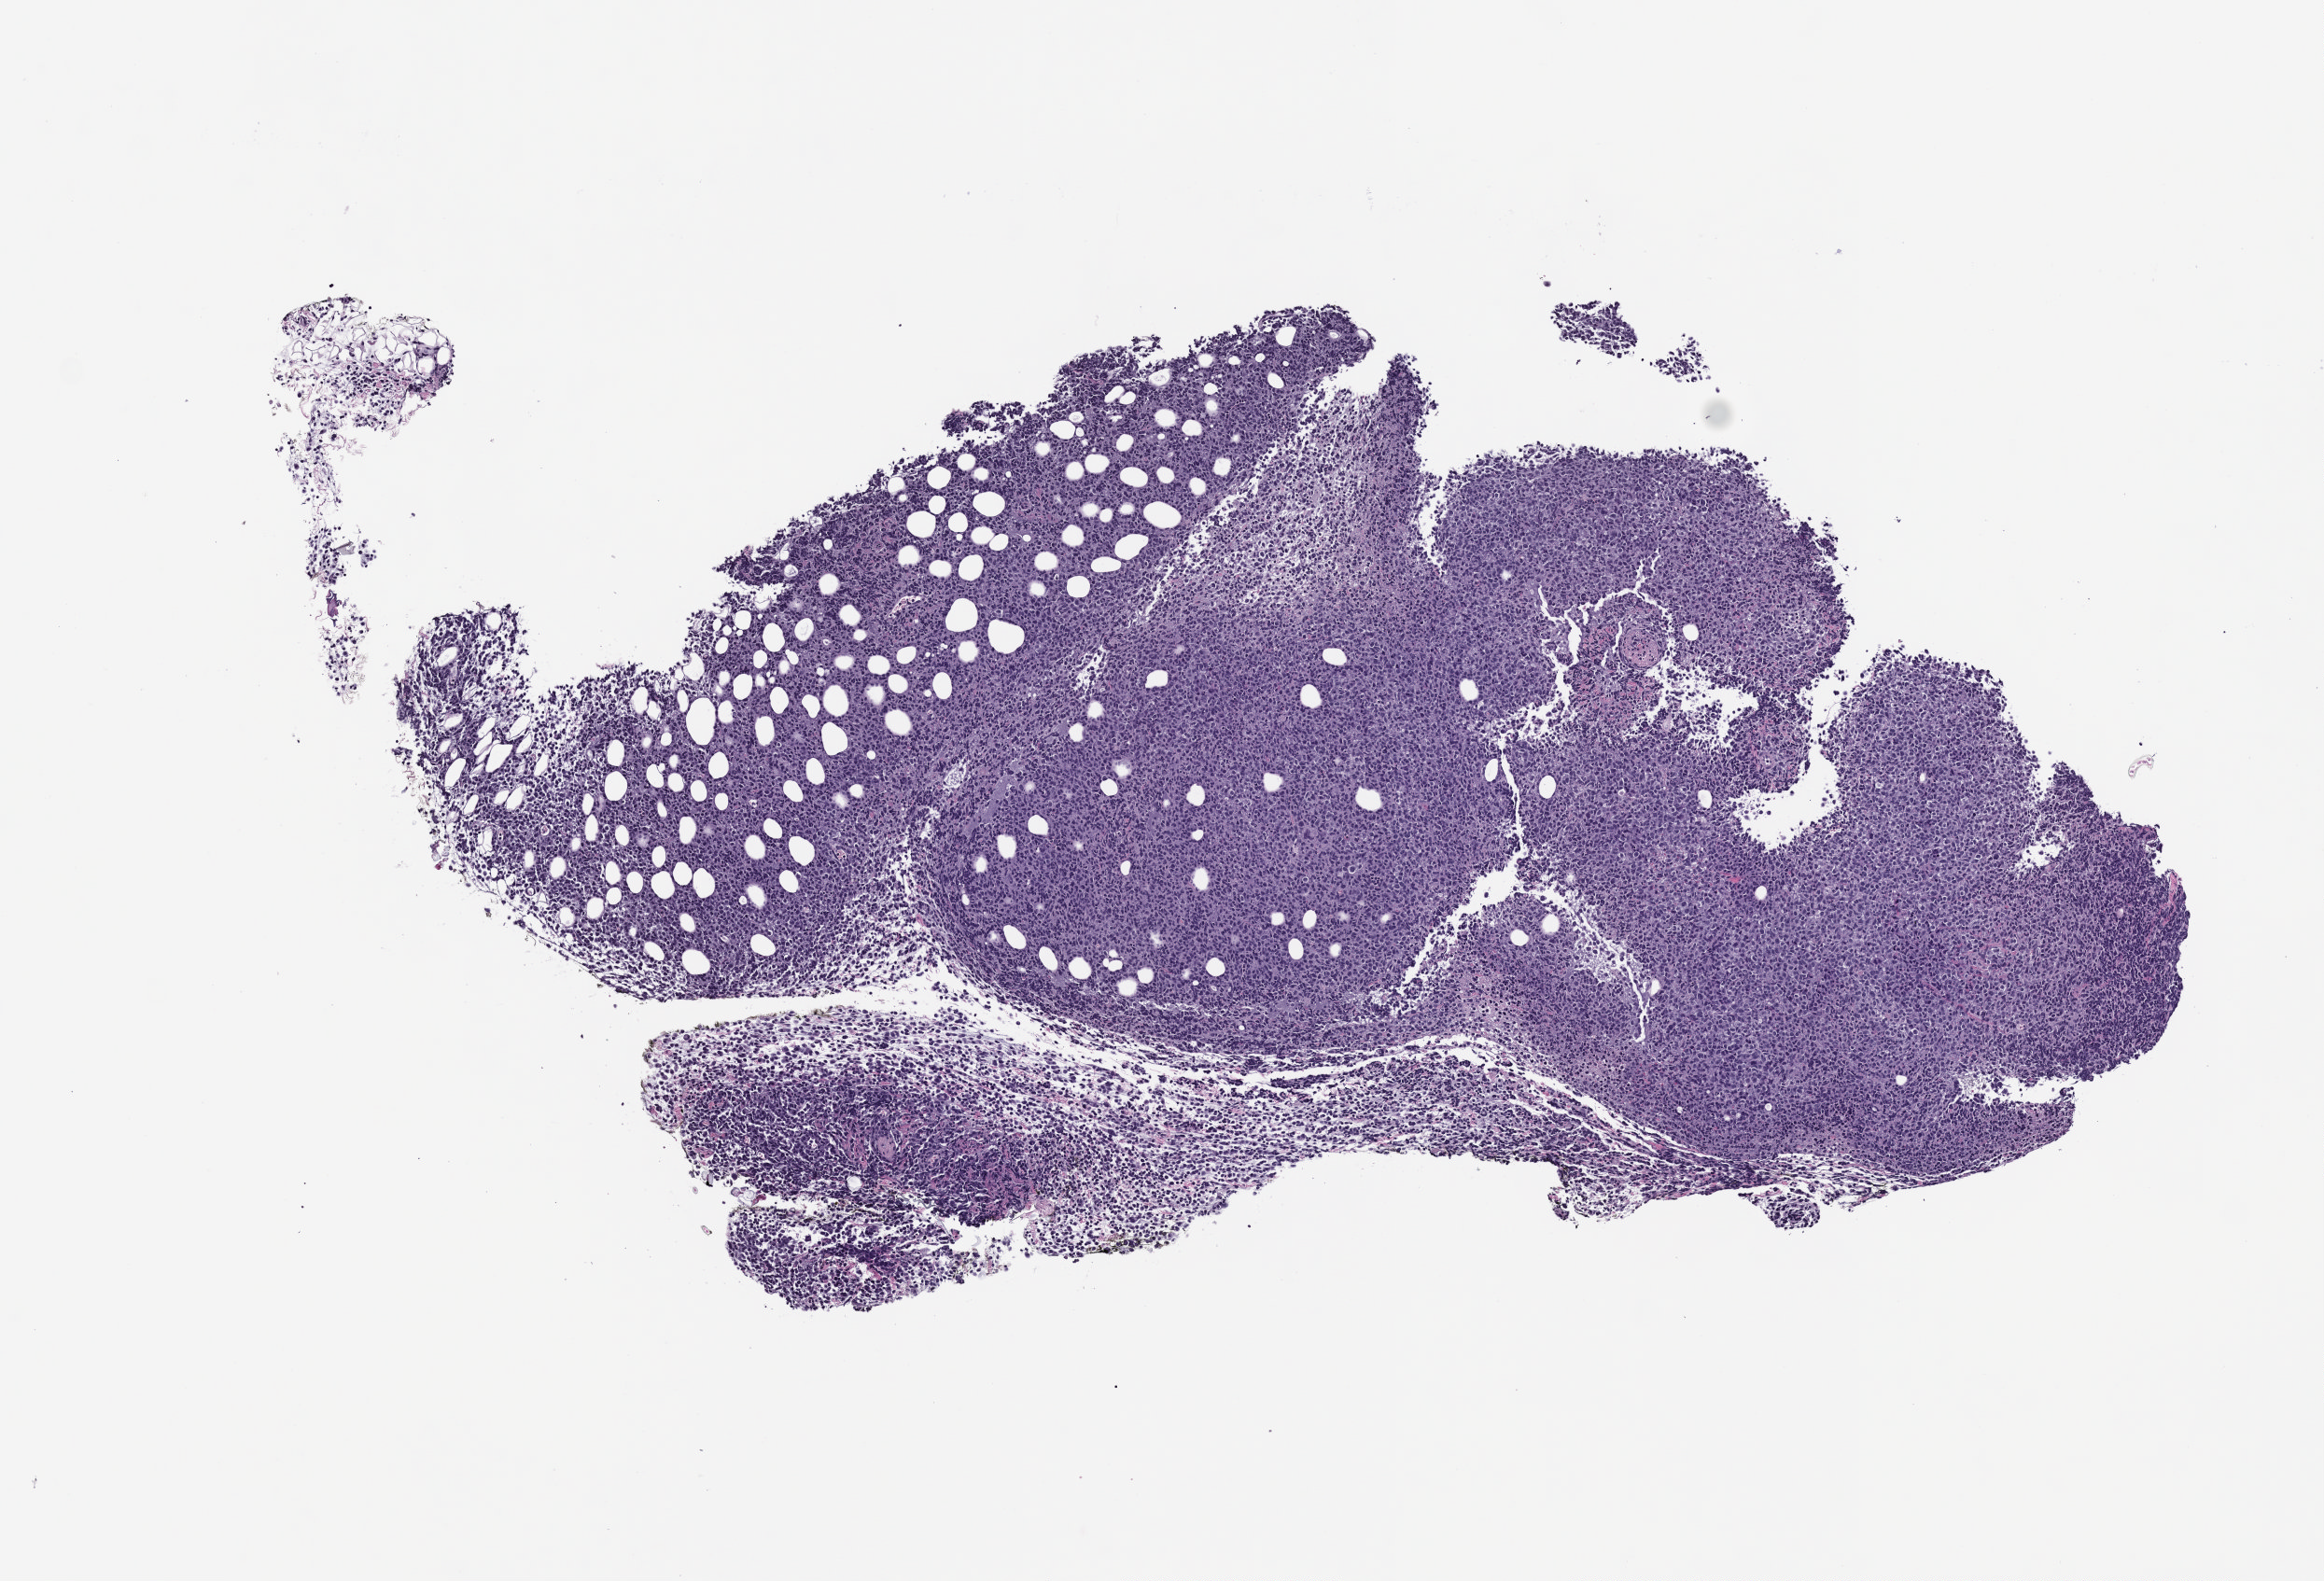
Whole-slide image, H&E: patient-derived xenograft (human tumor grown in a mouse) — shown as a low-resolution overview of the whole scanned area (about 5.0 x 3.4 mm).
Specimen: formalin-fixed, paraffin-embedded (FFPE) tissue.